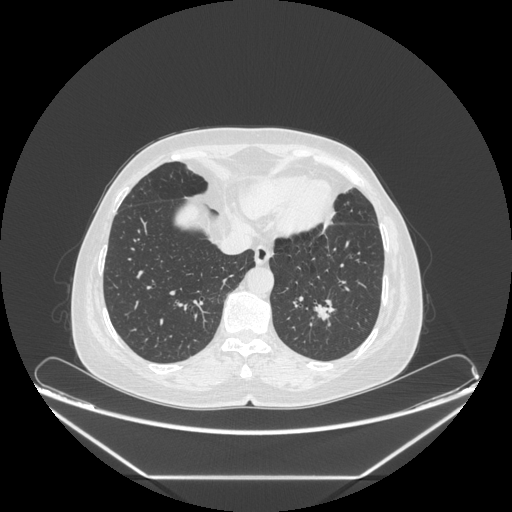
Chest CT, one axial slice; slice 69 of 241 in the series (ordered by position); reconstruction kernel STANDARD; lung window (W 1500 / L -600 HU); 512 × 512 image matrix, field of view 451 × 451 mm. Patient: female, 63 years. Case-level facts recorded for this patient, not image findings: clinical TNM (as recorded): T1c N0 M0.
Annotated regions visible in this slice (rectangle marked by the reading radiologist):
- lung tumour (recorded histology: adenocarcinoma): bounding box <315,295,342,333> (left, top, right, bottom; pixels)